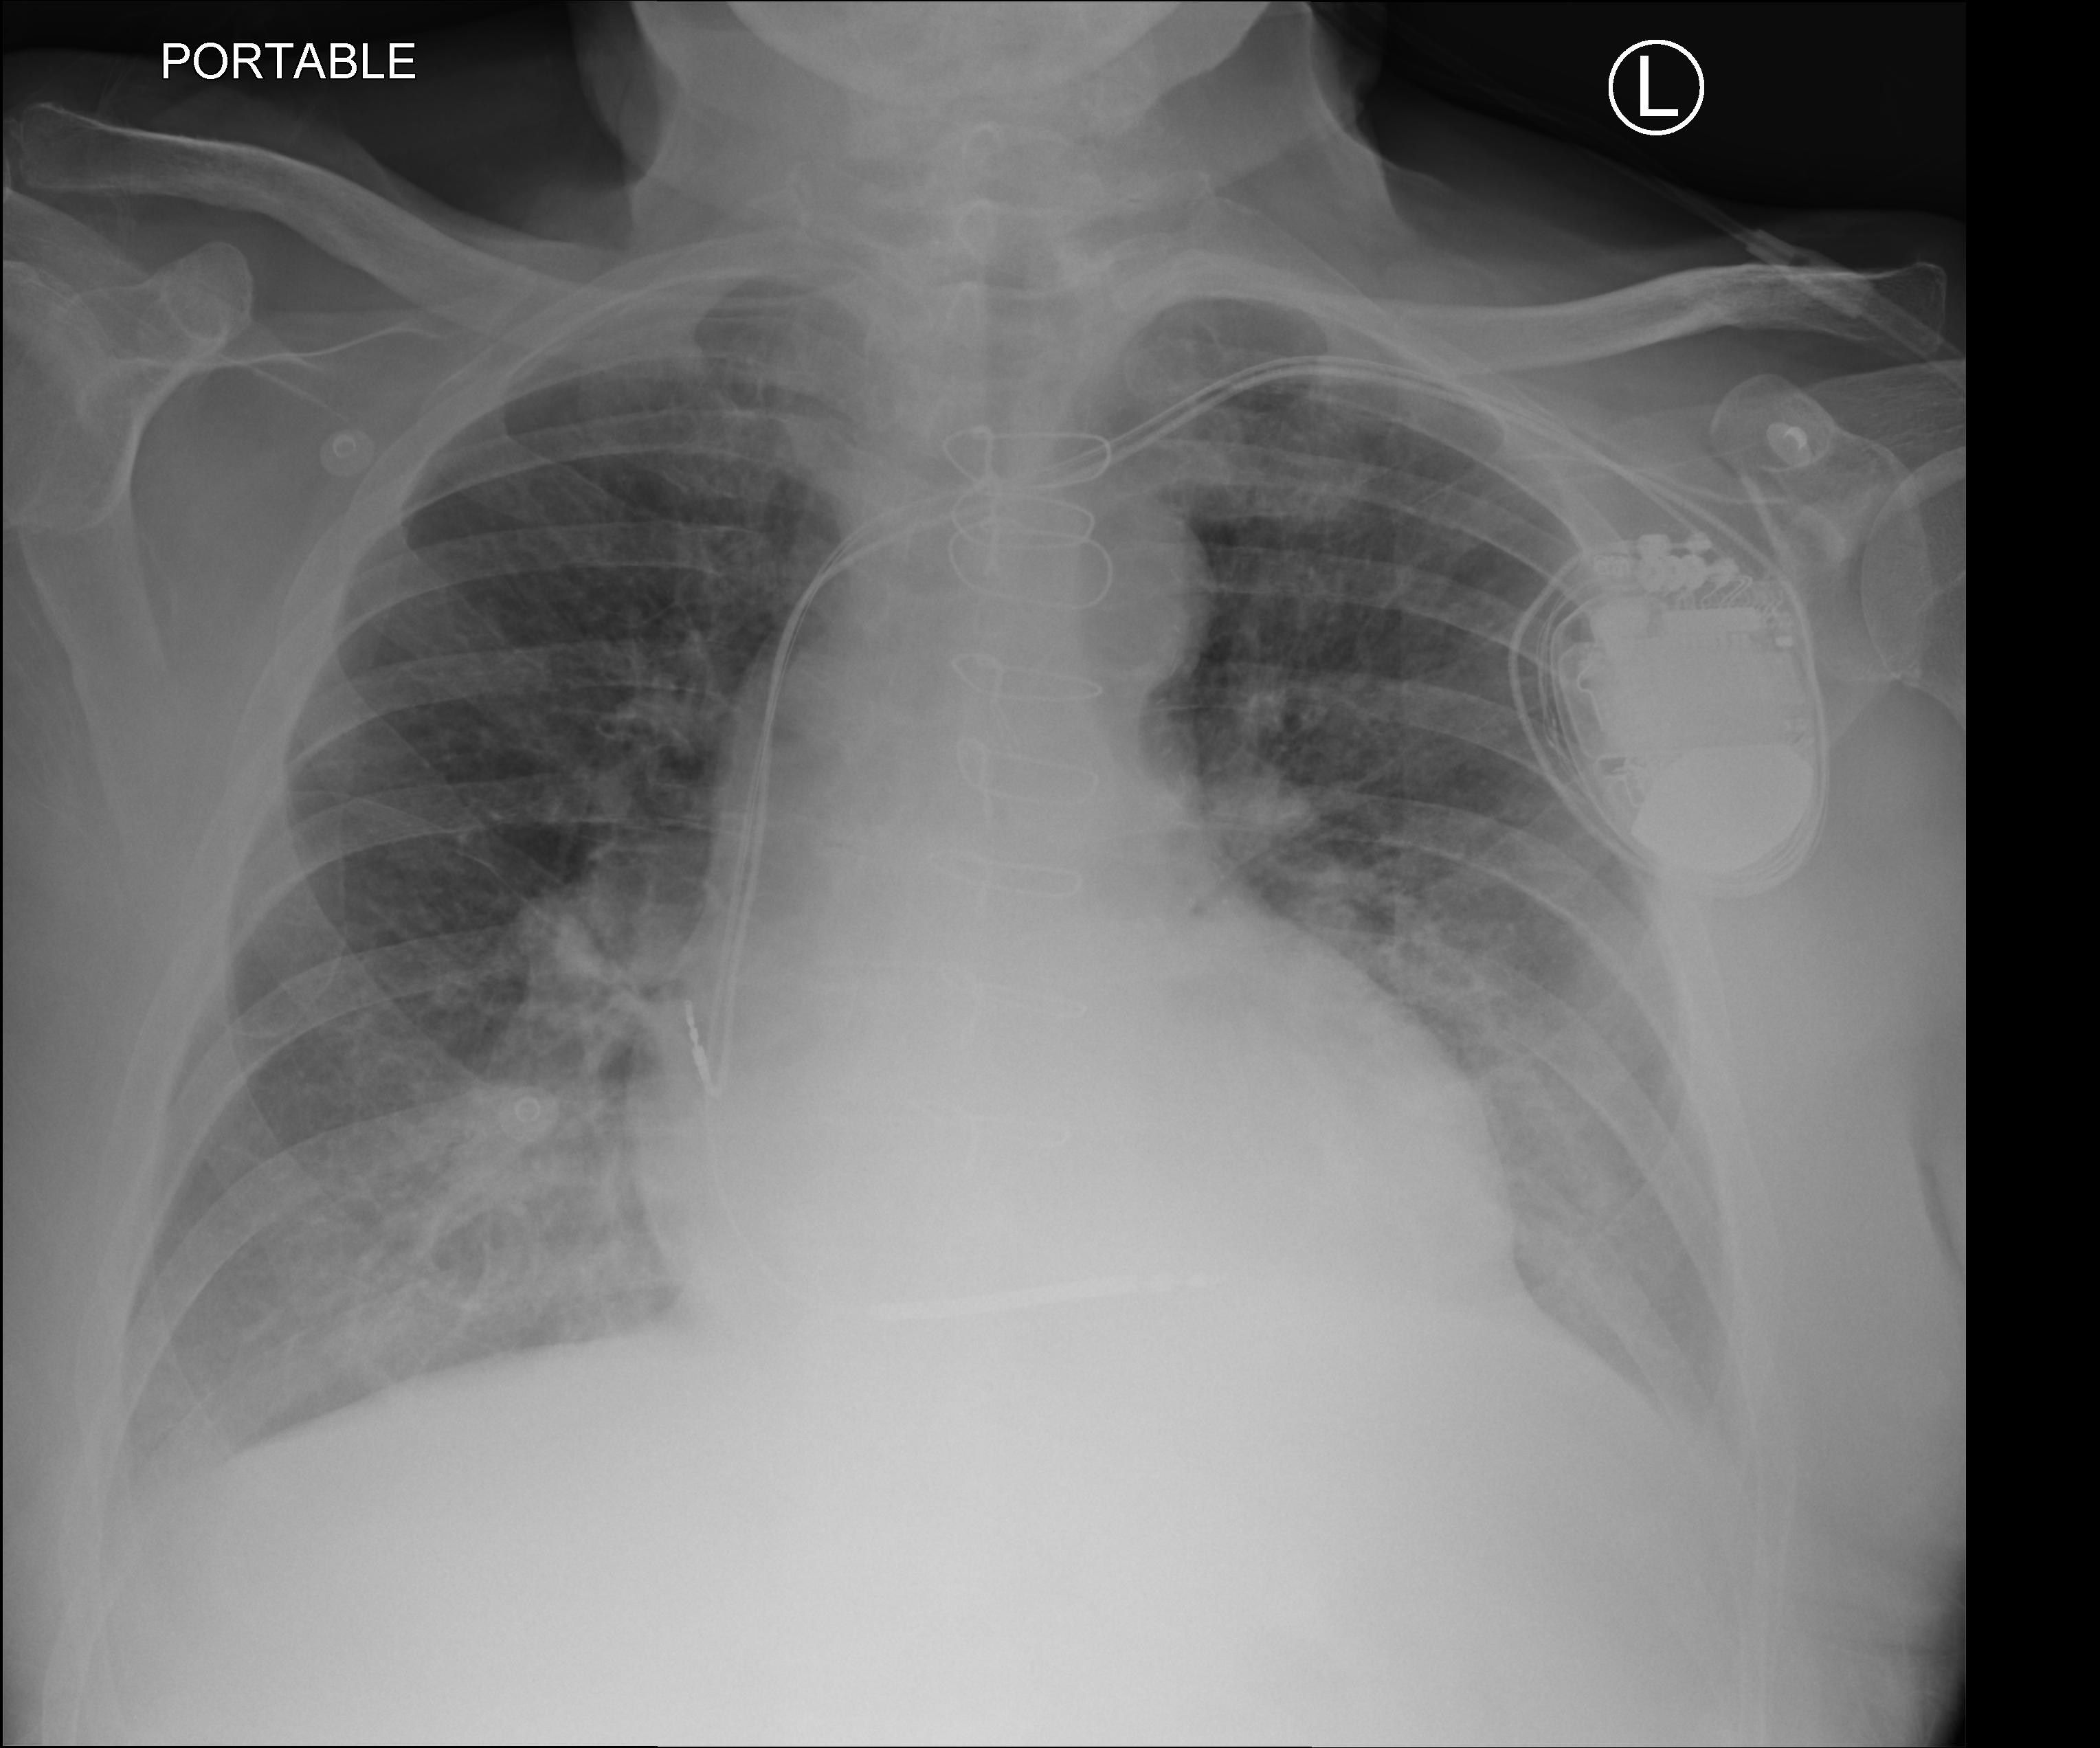
Chest radiograph. Male patient hospitalised with COVID-19, age 75–90 years.
Admission-level facts for this patient (not findings on this image; timing relative to this image not recorded):
- mechanically ventilated during this hospital stay: yes